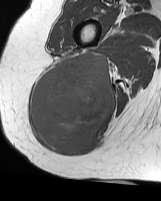
MRI of an extremity soft-tissue mass, one axial slice. Position 31 of 70 along the scan axis. MR volume resampled by the dataset authors to the PET/CT grid (not the native acquisition matrix). 3.27 mm slice thickness. 161 × 201 image matrix, field of view 157 × 196 mm. Female patient. From the clinical record (not read from this slice): histological type: synovial sarcoma; grade: intermediate; site of the primary tumour: right buttock.
Annotated regions visible in this slice (expert contour drawn on MRI and transferred to this co-registered scan by the dataset authors):
- gross tumour volume including surrounding oedema: bounding box [x1, y1, x2, y2] px = [31, 52, 116, 155]
- gross tumour volume (mass): [31, 52, 116, 155]